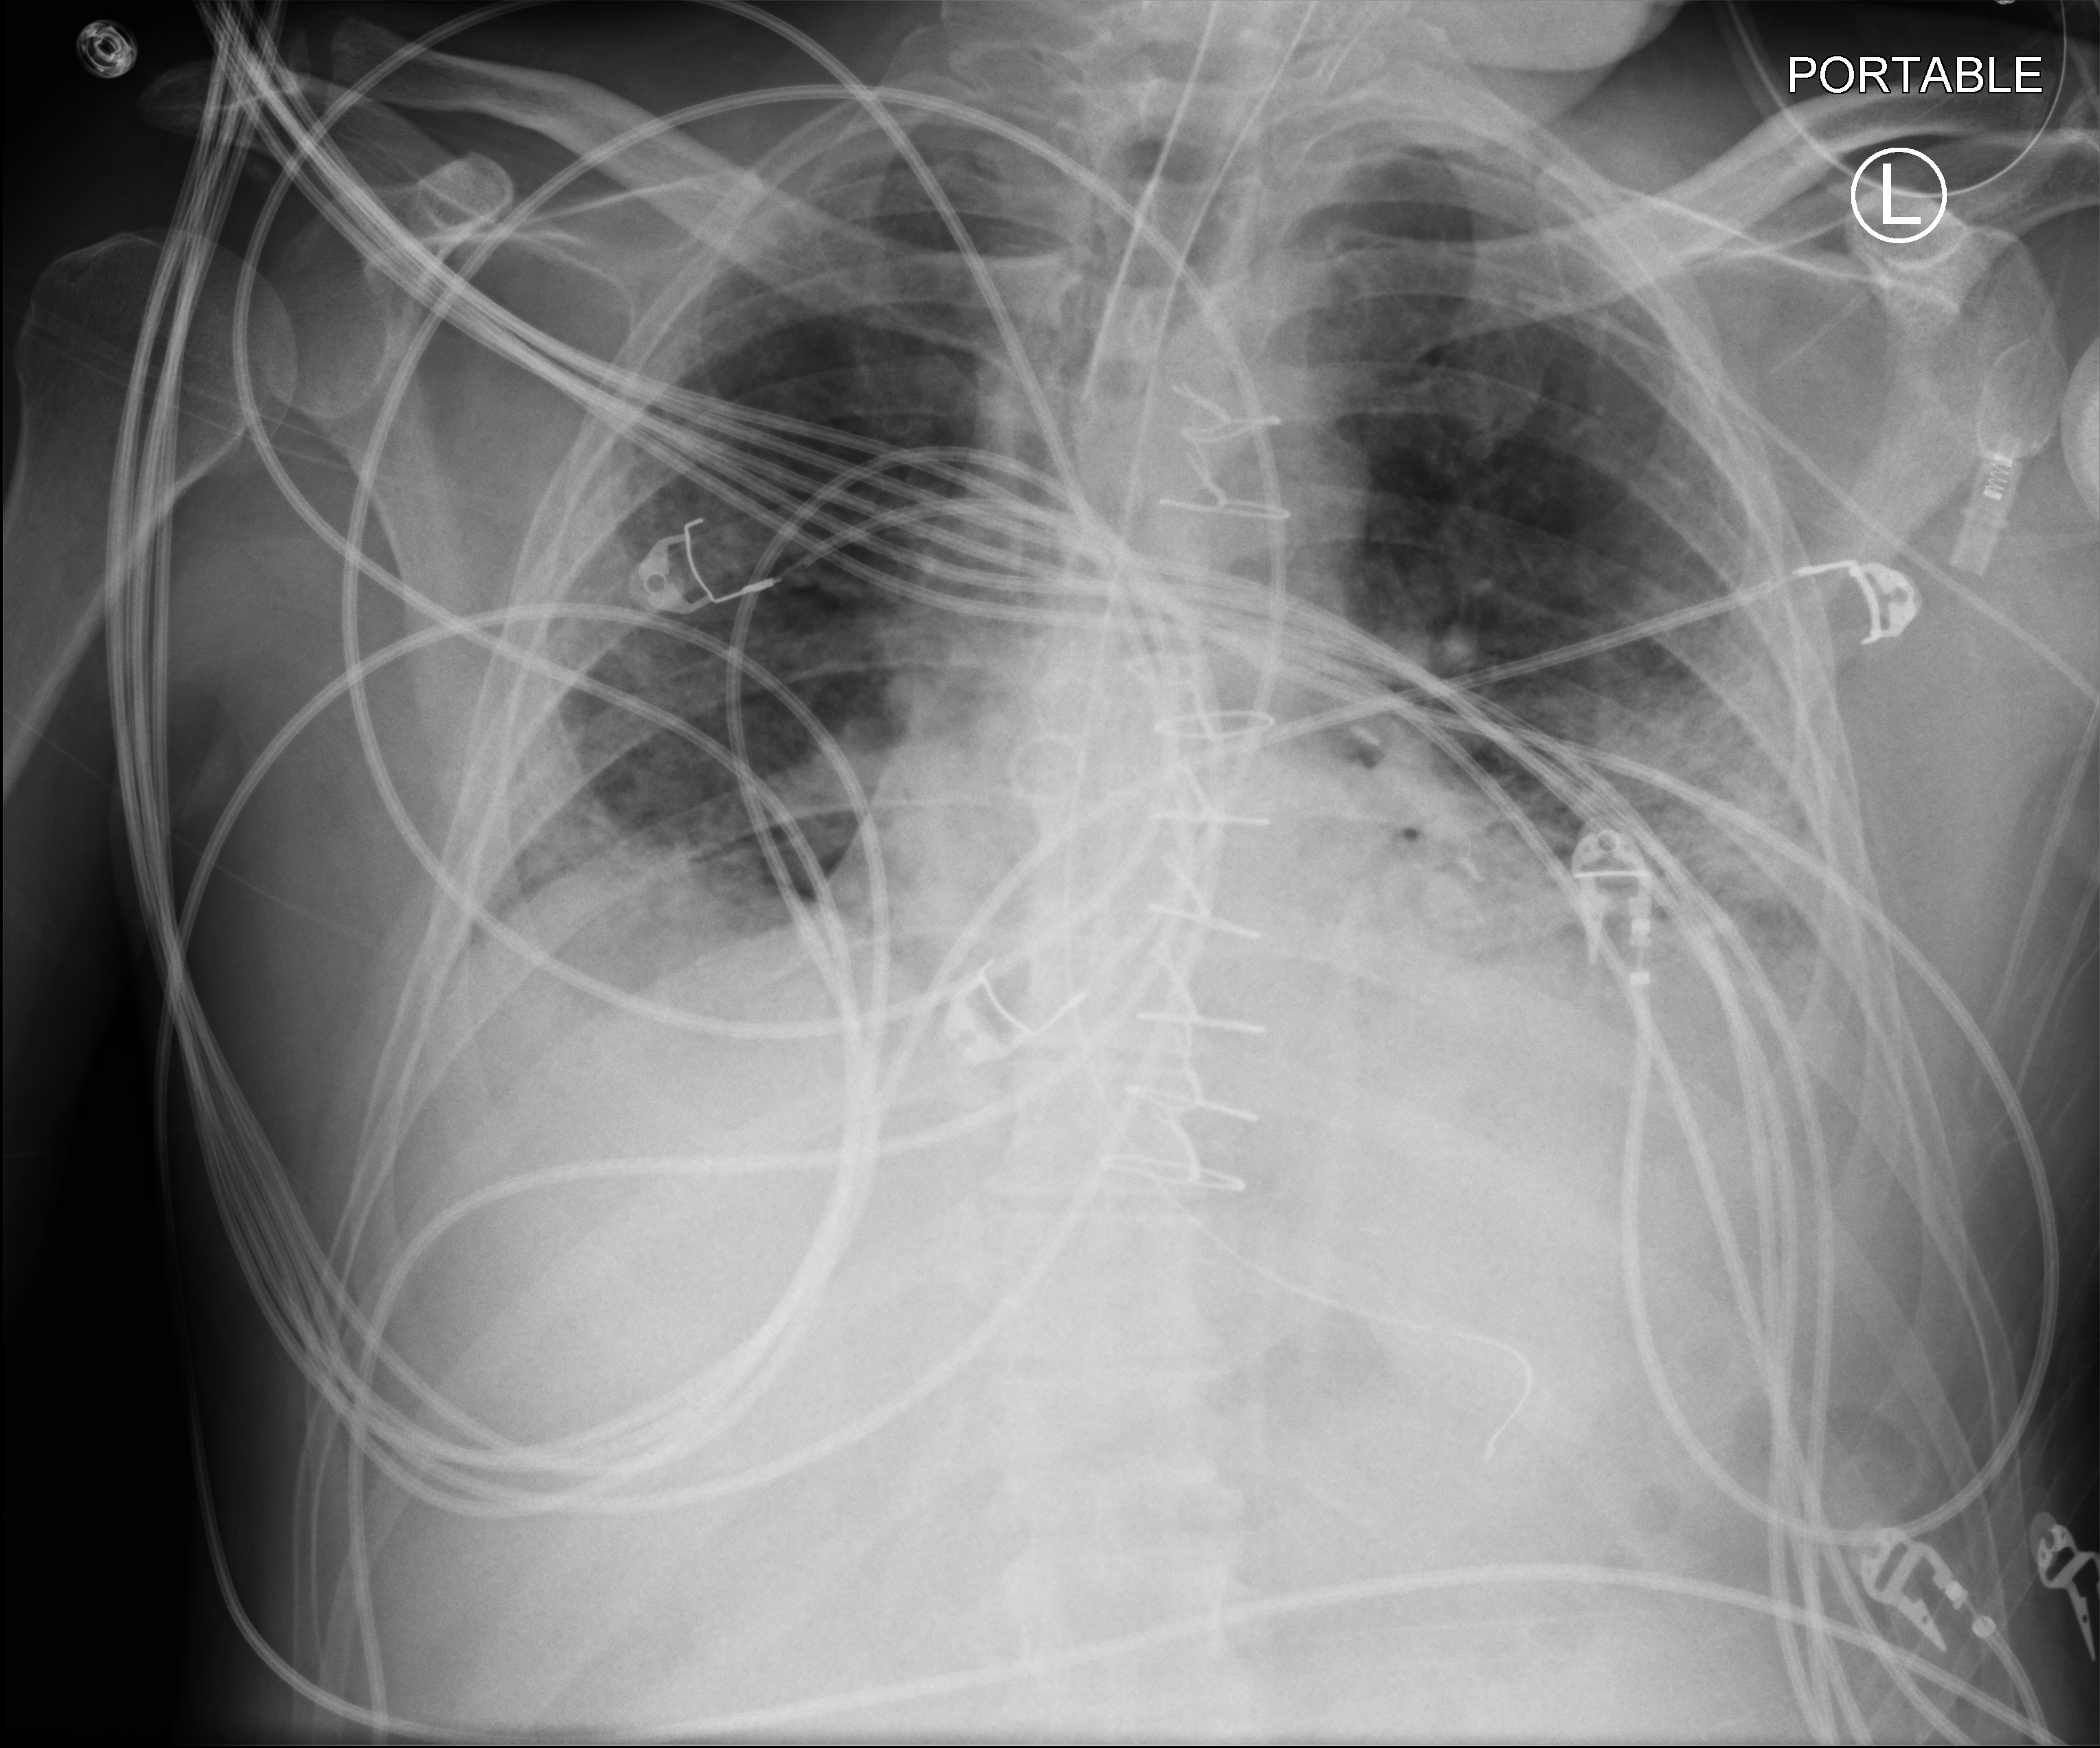
Portable chest radiograph. Patient hospitalised with COVID-19; male, aged 18–59 years.
Hospital-stay facts (about this admission, not read from this image; timing relative to this image not recorded):
- chronic kidney disease (admission record): no